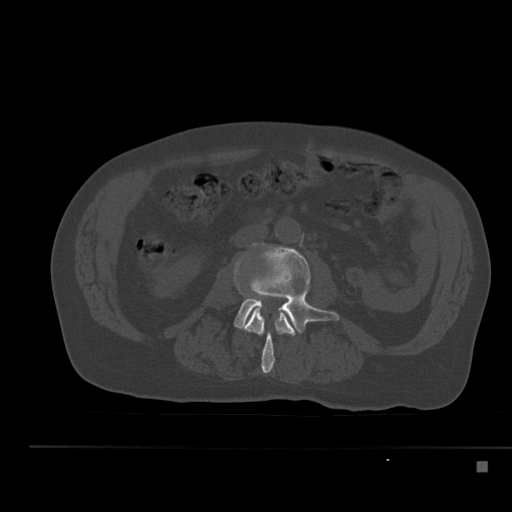
CT including the spine, one axial slice; reconstruction kernel Br40s; bone window (W 1800 / L 400 HU); 512 × 512 image matrix, field of view 408 × 408 mm. Male patient, age 70 years. Case-level facts recorded for this patient, not image findings: primary cancer: renal.
Annotated regions visible in this slice (semi-automatic segmentation, software-assisted and operator-edited):
- L2 vertebra: box from (x=237, y=284) to (x=296, y=374) px
- L3 vertebra: (x=234, y=247)–(x=340, y=334)